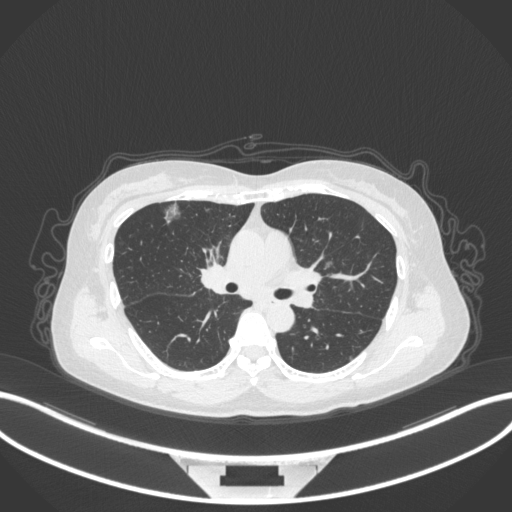
Chest CT, one axial slice. Slice 197 of 317 in the series (ordered by position). Lung window (W 1500 / L -600 HU). 512 × 512 image matrix, field of view 400 × 400 mm. Female patient, age 61 years. From the clinical record (not read from this slice): clinical TNM (as recorded): T1b N0 M0; histopathological grade: G1.
Annotated regions visible in this slice (rectangle marked by the reading radiologist):
- lung tumour (recorded histology: adenocarcinoma): box from (x=160, y=195) to (x=184, y=228) px